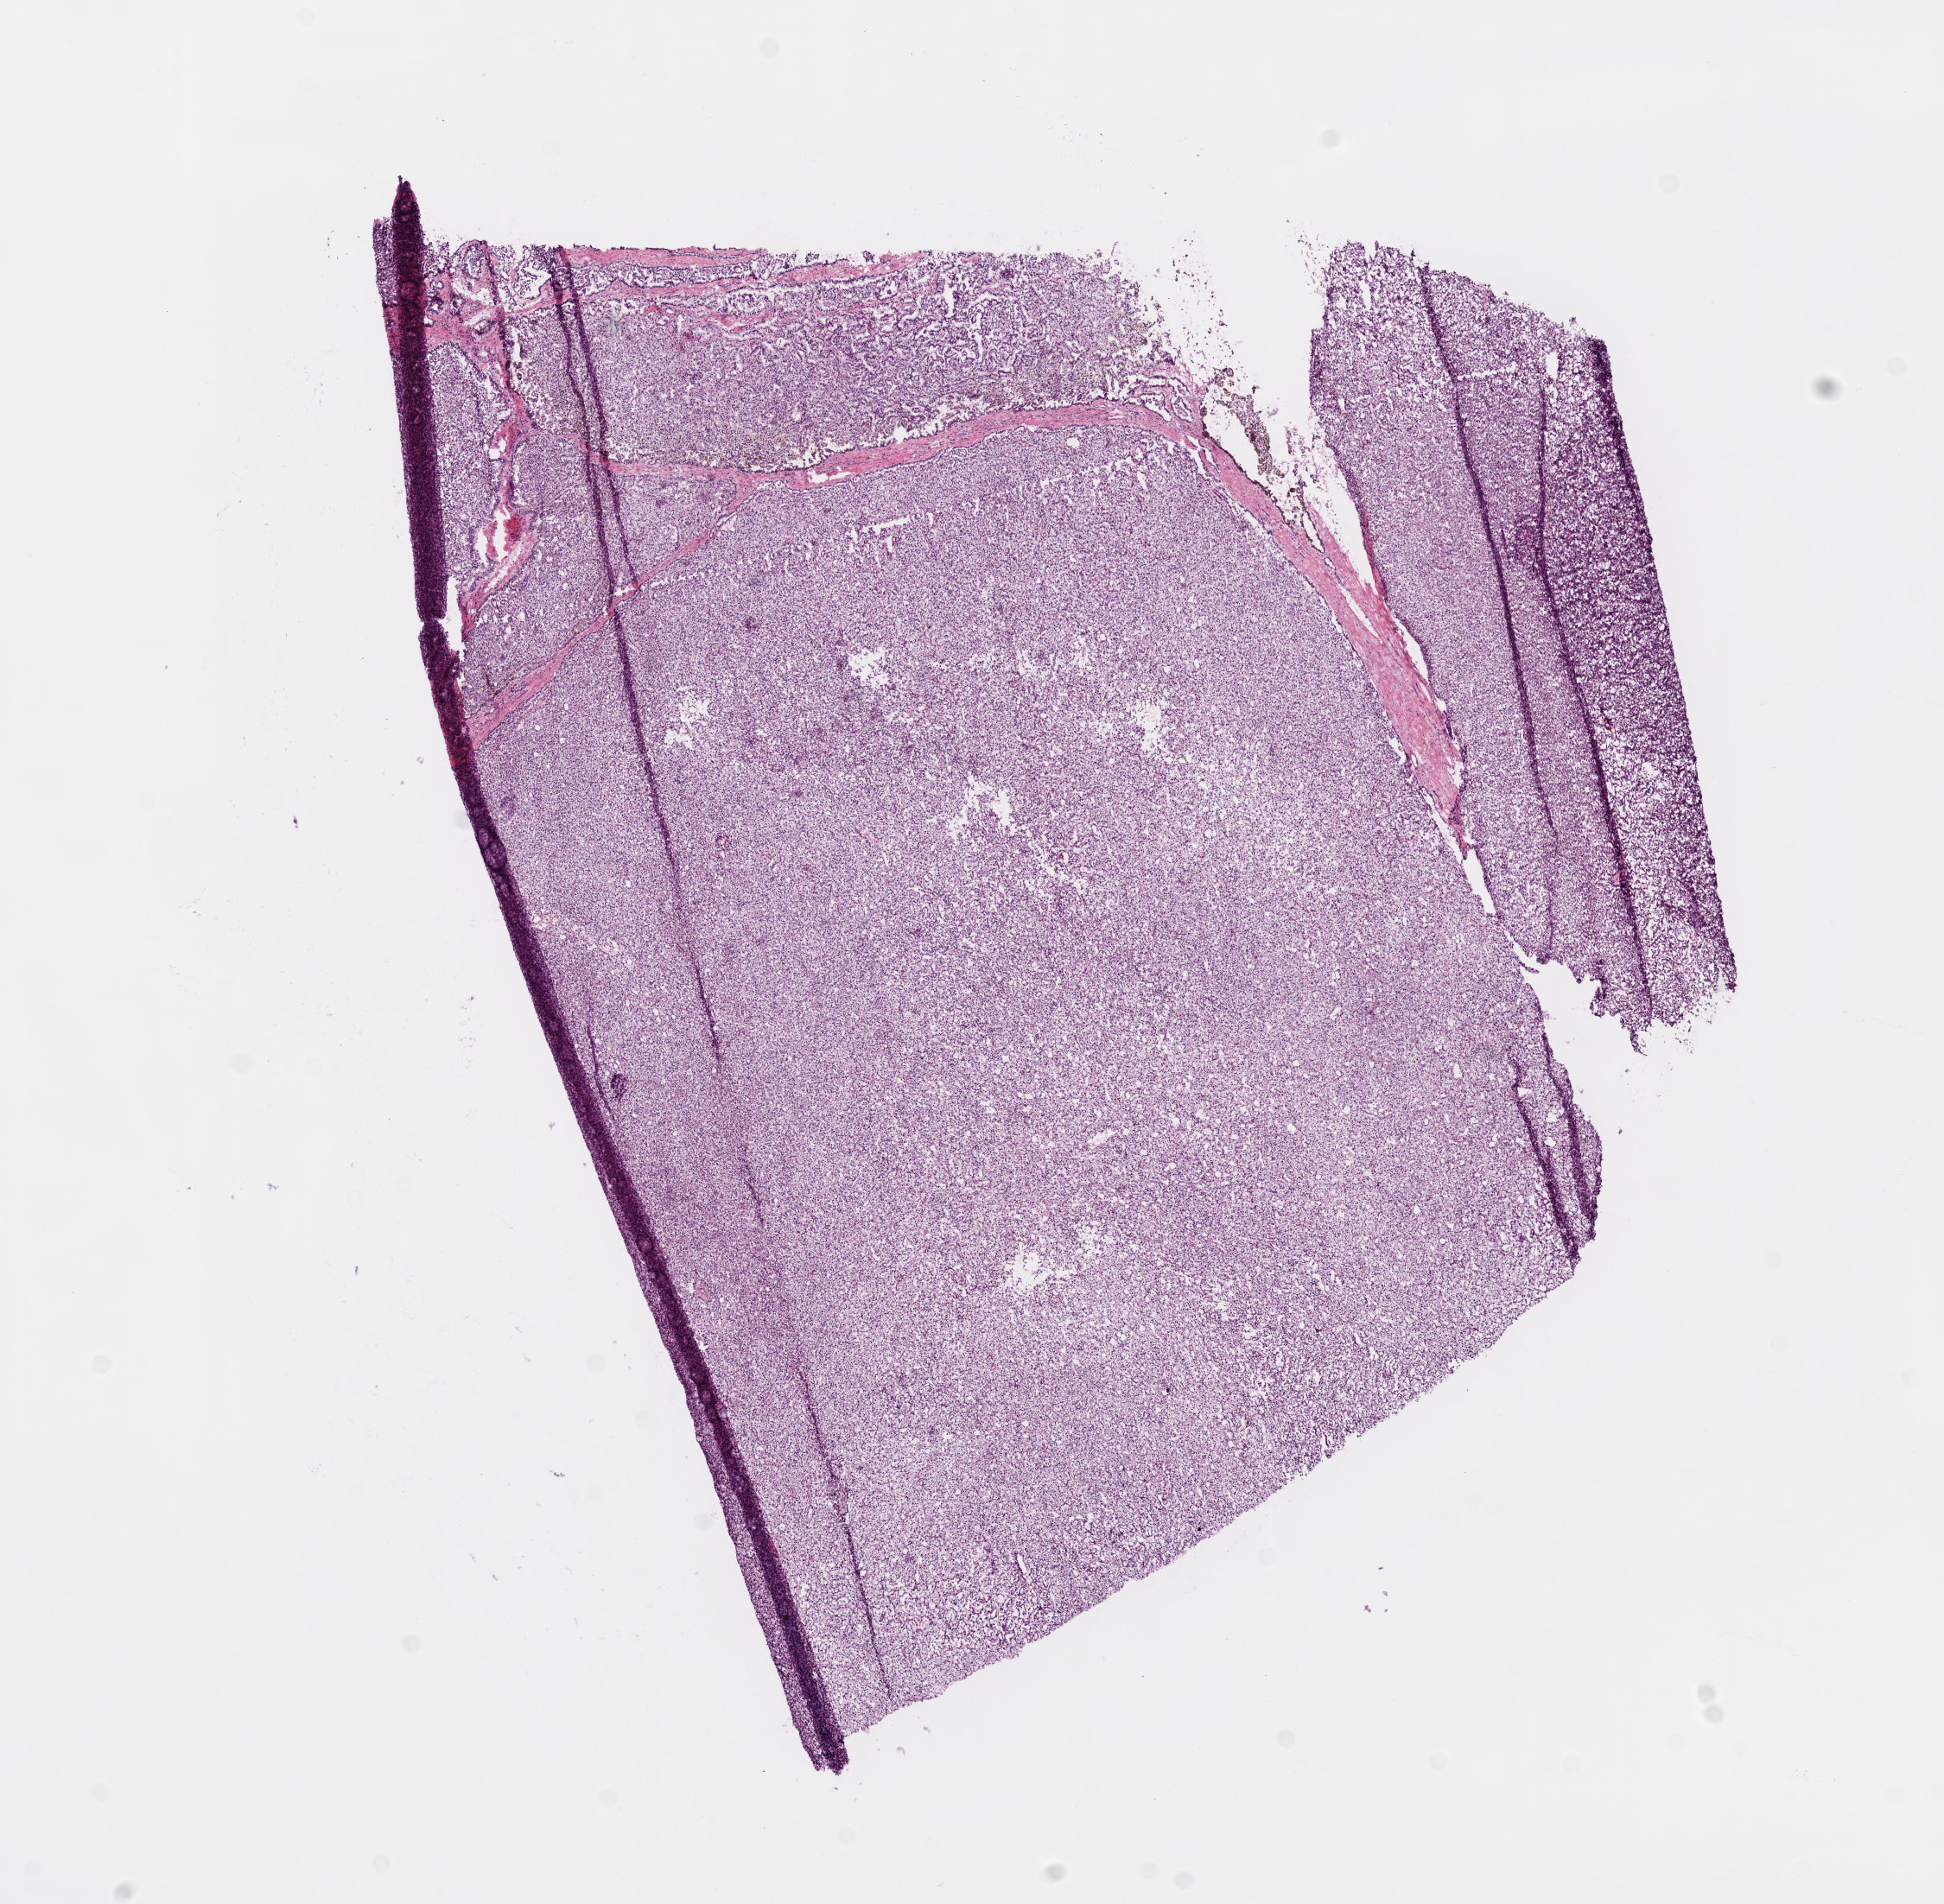
Whole-slide histology image, H&E-stained, a low-resolution overview of the entire scanned area, about 9.0 x 8.8 mm, frozen section from the top of the tissue portion, sample: primary tumour, kidney. Male, age 50 years at initial diagnosis. Histologic grade: G2 (moderately differentiated). Slide review estimates, as recorded: tumour cells 90%, tumour nuclei 85%, normal cells 5%, stromal cells 5%, necrosis 0%.
AJCC pathologic stage: II. Histologic diagnosis: Clear cell adenocarcinoma, NOS.